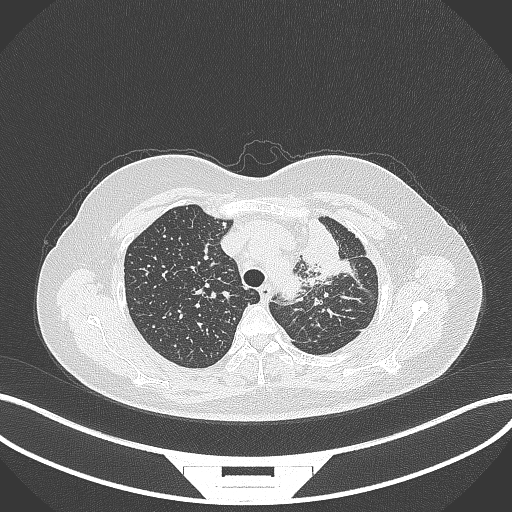
Chest CT, one axial slice; reconstruction kernel B70f; 120 kVp; lung window (W 1500 / L -600 HU); 512 × 512 image matrix, field of view 400 × 400 mm. Patient: female, 49 years. From the clinical record (not read from this slice): clinical TNM (as recorded): T1c N0 M1.
Annotated regions visible in this slice (rectangle marked by the reading radiologist):
- lung tumour (recorded histology: adenocarcinoma): box from (x=298, y=214) to (x=353, y=279) px